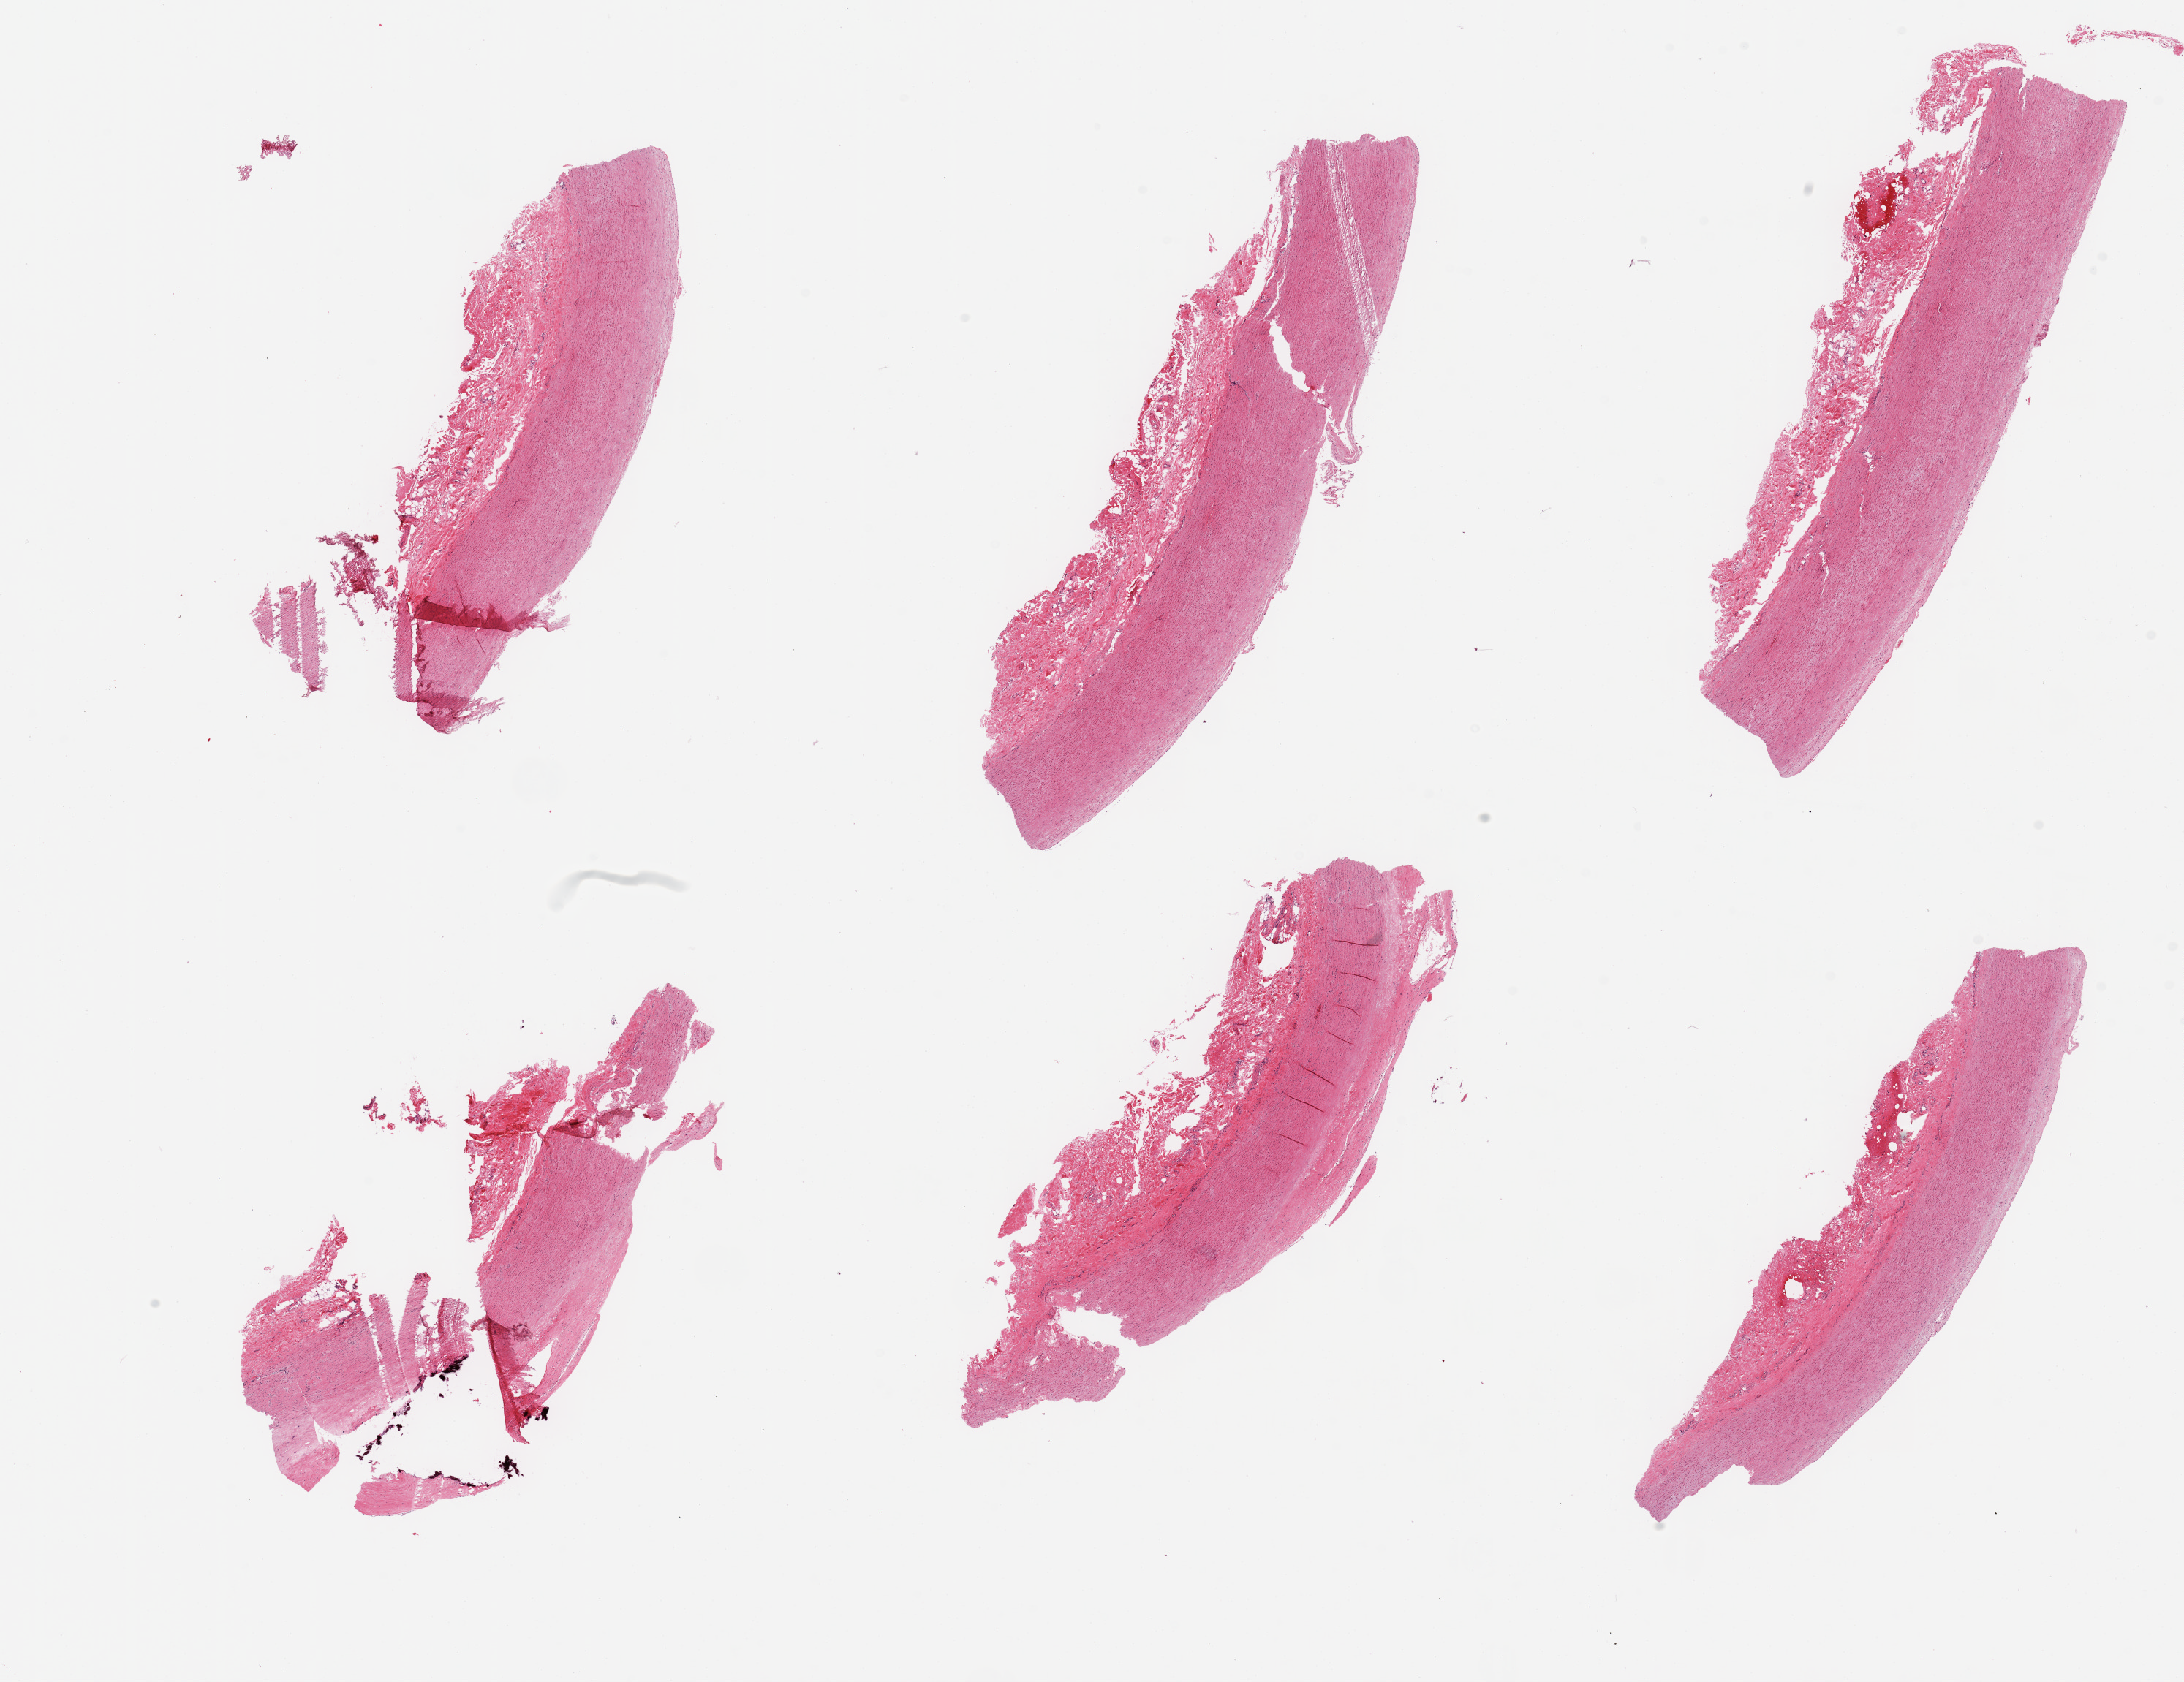
Hematoxylin and eosin (H&E) whole-slide image — a low-resolution overview of the entire scanned area, about 23.6 x 18.2 mm, PAXgene-fixed, paraffin-embedded tissue, sampled site (target tissue): aorta, tissue donor sample. Donor: male.
Pathologist's review note for this sample: 6 pieces, minimal atherosis; adherent serosa and fat up to ~1mm.